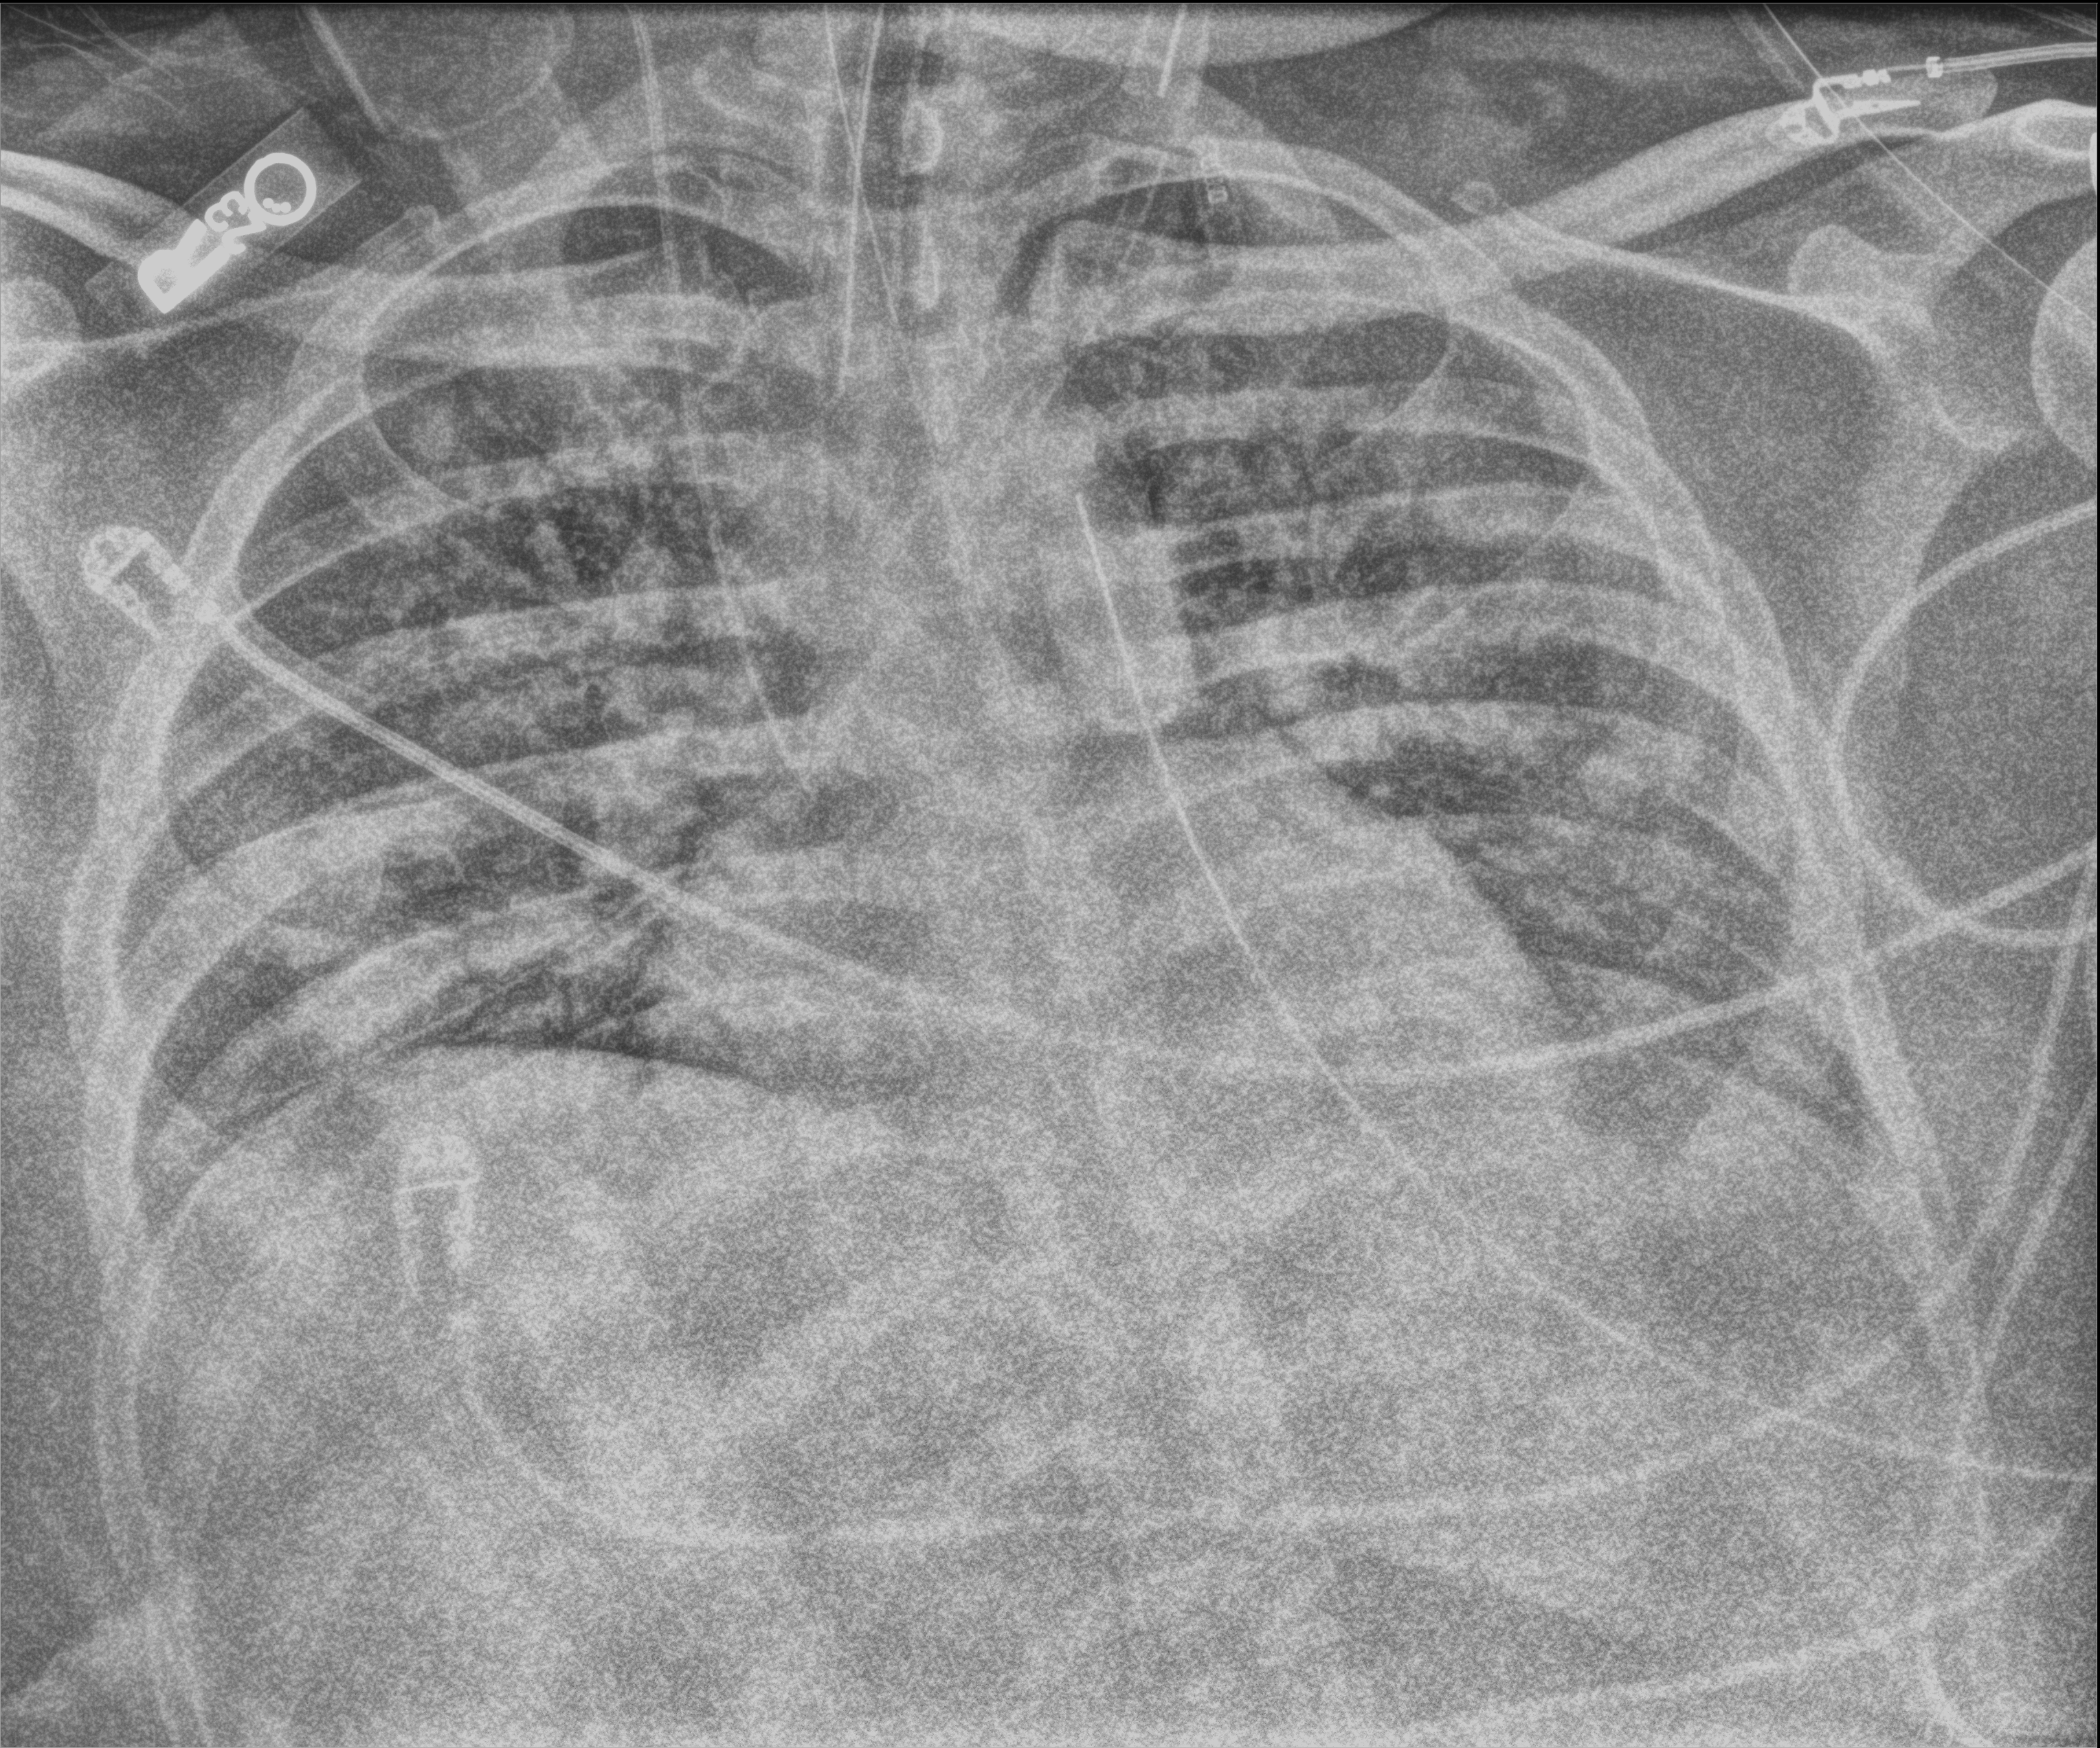
Chest X-ray (portable); anteroposterior (AP) projection. Male patient hospitalised with COVID-19, age 18–59 years.
Hospital-stay facts (about this admission, not read from this image; timing relative to this image not recorded): other chronic lung disease (admission record): yes; admitted to intensive care during this hospital stay: yes; diabetes (admission record): yes.